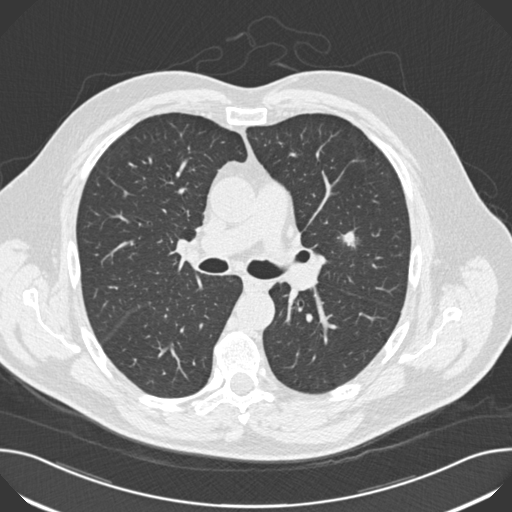
Low-dose screening chest CT, one axial slice. Position 106 of 174 along the scan axis. Lung window (W 1500 / L -600 HU). 2 mm slice thickness. 512 × 512 image matrix.
Structures marked on this image (manually delineated by an expert):
- lesion 1 (tumor, upper lobe of left lung): box from (x=338, y=231) to (x=355, y=247) px